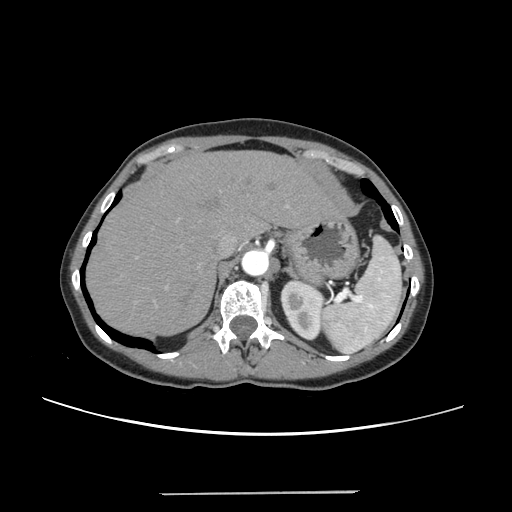
Contrast-enhanced abdominal CT, one axial slice; position 186 of 240 along the scan axis; 120 kVp; soft-tissue window (W 400 / L 40 HU); 512 × 512 image matrix, field of view 371 × 371 mm. Female patient, age 60 years. From the clinical record (not read from this slice): diagnosis: colorectal cancer liver metastases, imaged before liver resection.
Outlined on this slice (expert manual segmentation):
- hepatic veins: bounding box (x1, y1, x2, y2) in pixels: (220, 234, 236, 254)
- liver: (88, 152, 337, 336)
- planned liver remnant (the part of the liver to remain after resection): (88, 152, 337, 336)
- portal vein (with intrahepatic branches): (165, 205, 288, 288)